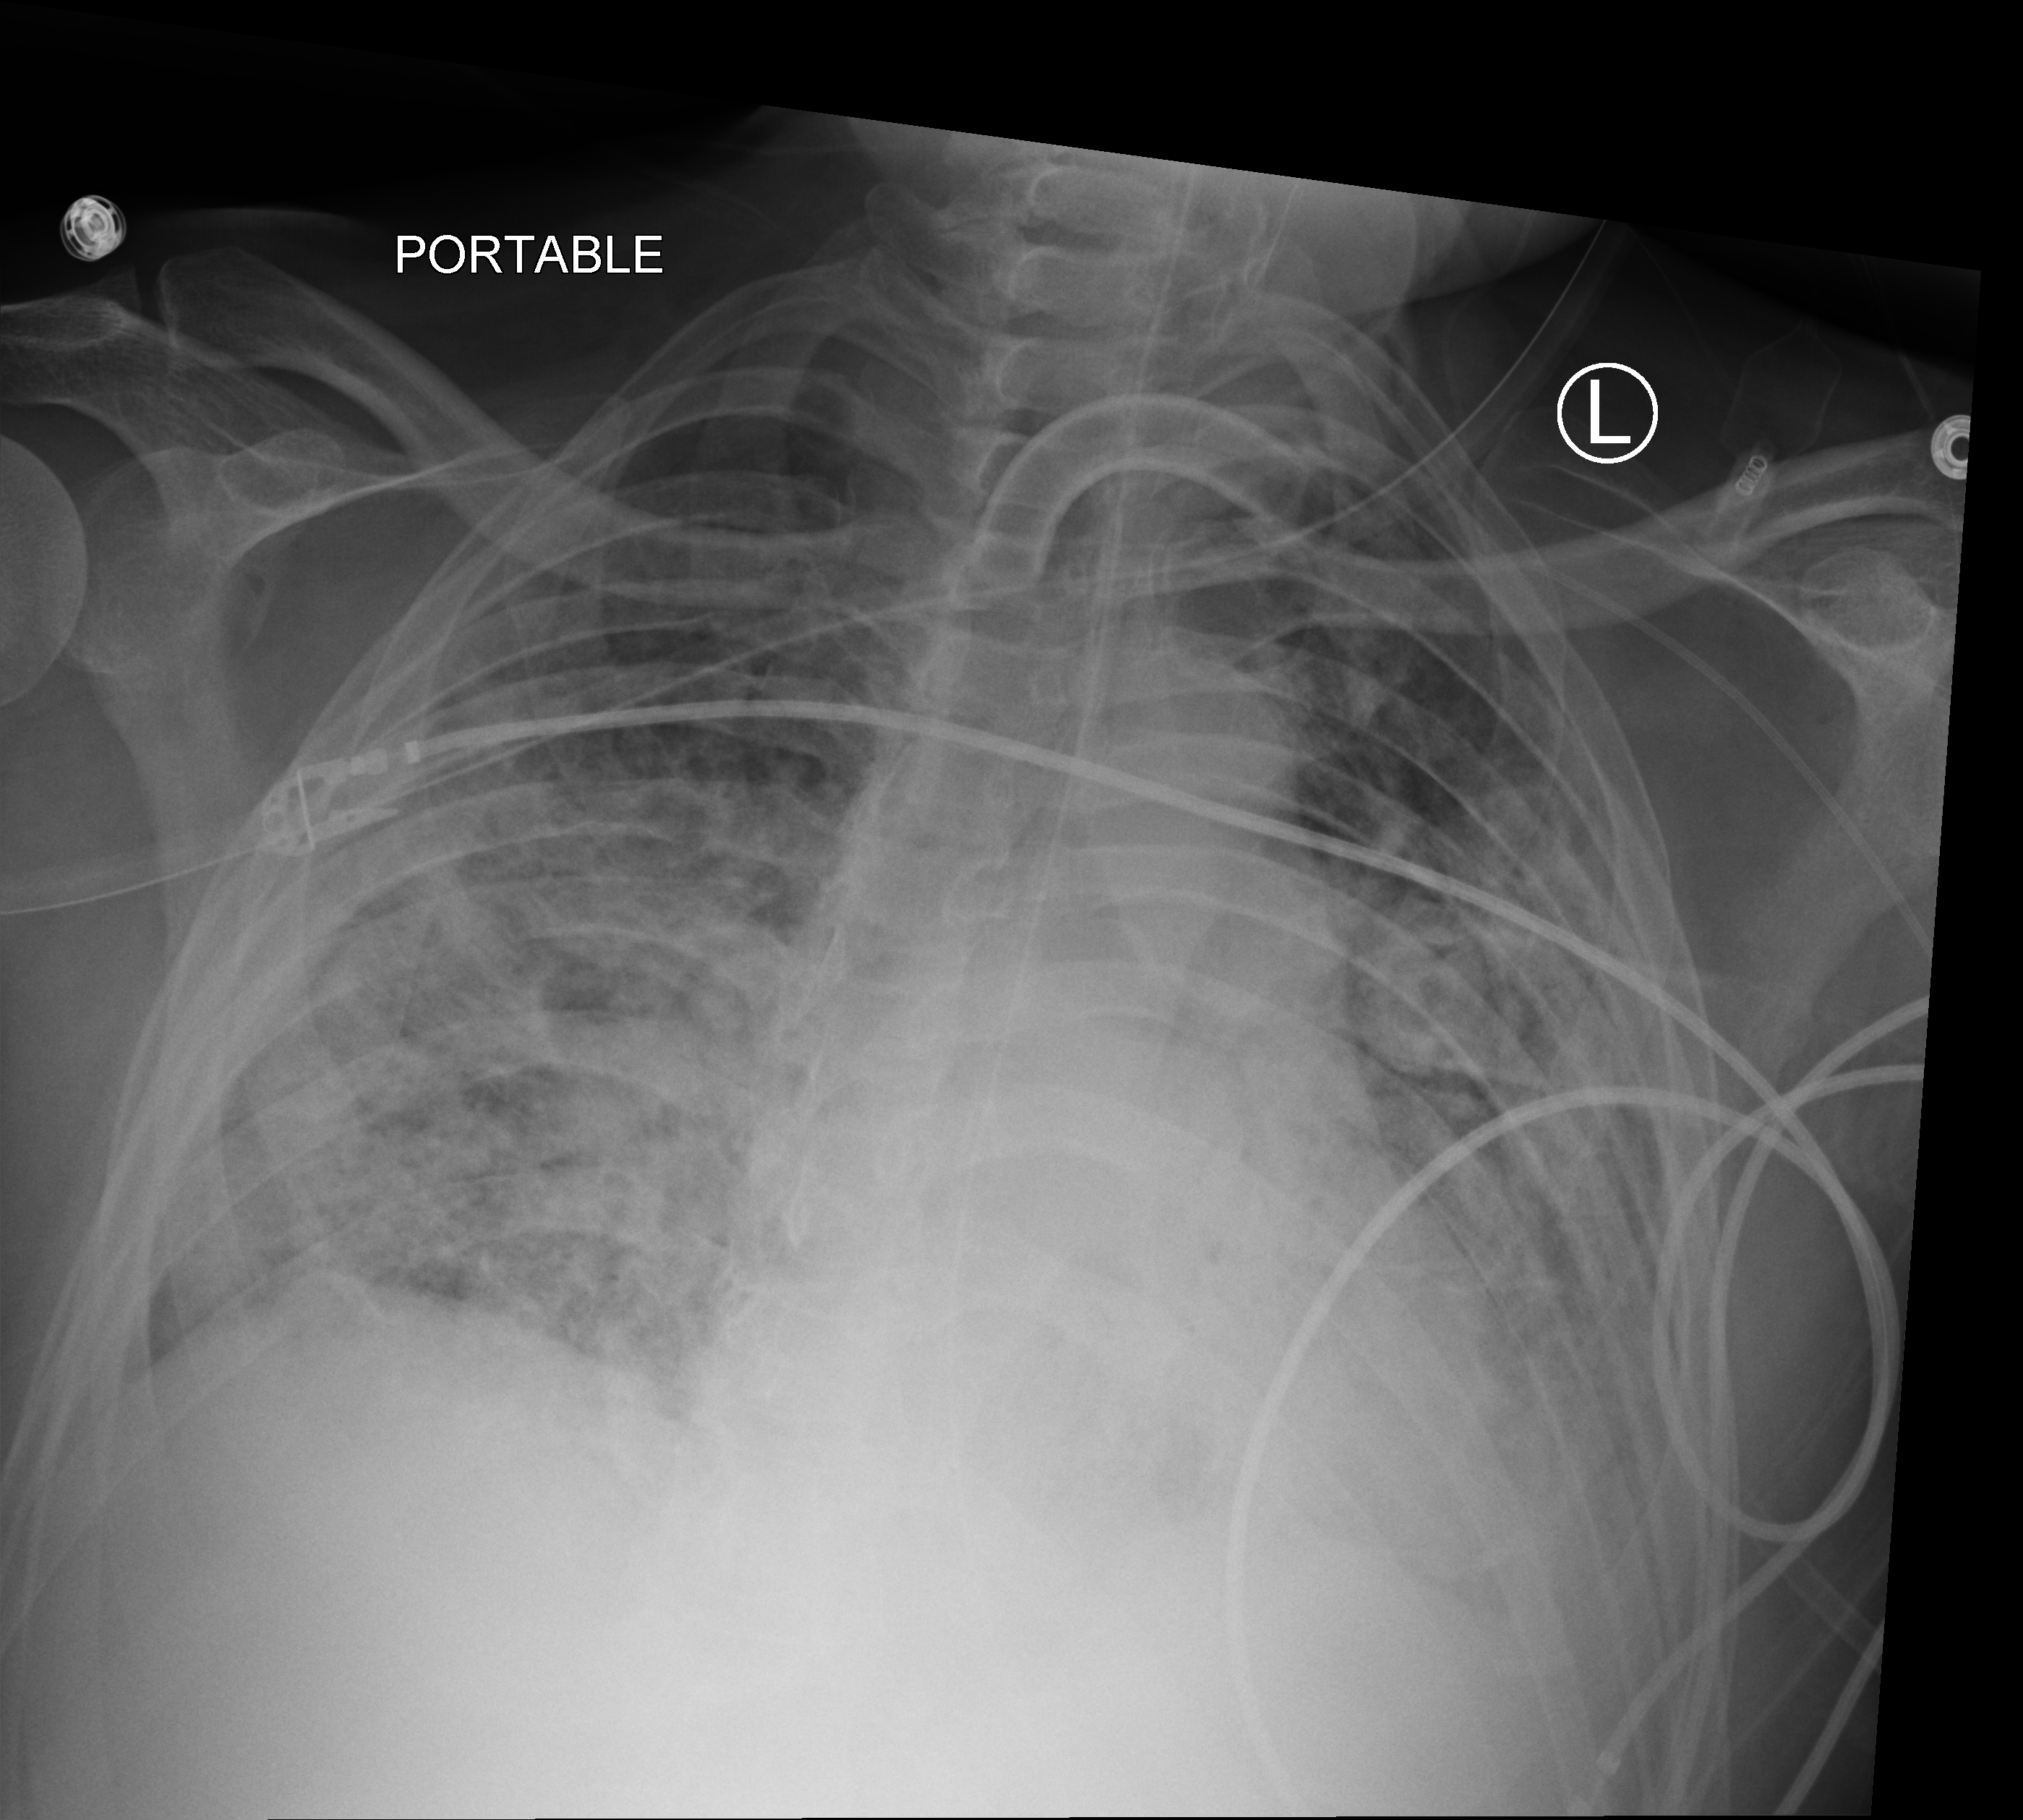
Chest X-ray (portable); anteroposterior (AP) projection. Patient hospitalised with COVID-19; male, aged 18–59 years.
Admission-level facts for this patient (not findings on this image; timing relative to this image not recorded): admitted to intensive care during this hospital stay: yes.